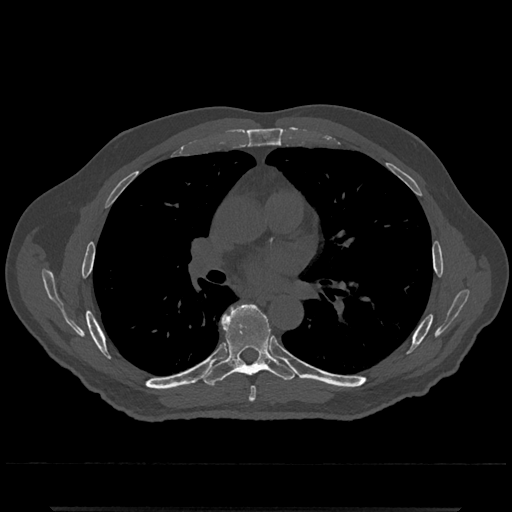
CT including the spine, one axial slice. Position 735 of 797 along the scan axis. Reconstruction kernel Br40s/3. 120 kVp. Bone window (W 1800 / L 400 HU). 0.5 mm slice thickness. 512 × 512 image matrix, field of view 393 × 393 mm. Male patient, age 67 years. Case-level facts recorded for this patient, not image findings: primary cancer: prostate.
Annotated regions visible in this slice (semi-automatic segmentation, software-assisted and operator-edited):
- T6 vertebra: bounding box [x1, y1, x2, y2] px = [249, 387, 256, 402]
- T7 vertebra: [203, 304, 296, 386]